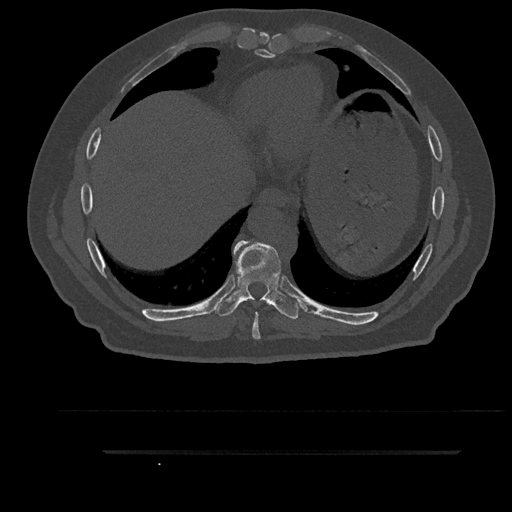
CT including the spine, one axial slice; slice 440 of 797 in the series (ordered by position); reconstruction kernel Br40s/3; 120 kVp; bone window (W 1800 / L 400 HU); 0.5 mm slice thickness; 512 × 512 image matrix, field of view 432 × 432 mm. Patient: male, 63 years. Case-level facts recorded for this patient, not image findings: primary cancer: renal; vertebrae with lytic lesions (as recorded): T8.
Annotated regions visible in this slice (semi-automatic segmentation, software-assisted and operator-edited):
- T8 vertebra: bounding box [x1, y1, x2, y2] px = [234, 241, 276, 340]
- T9 vertebra: [213, 240, 300, 319]